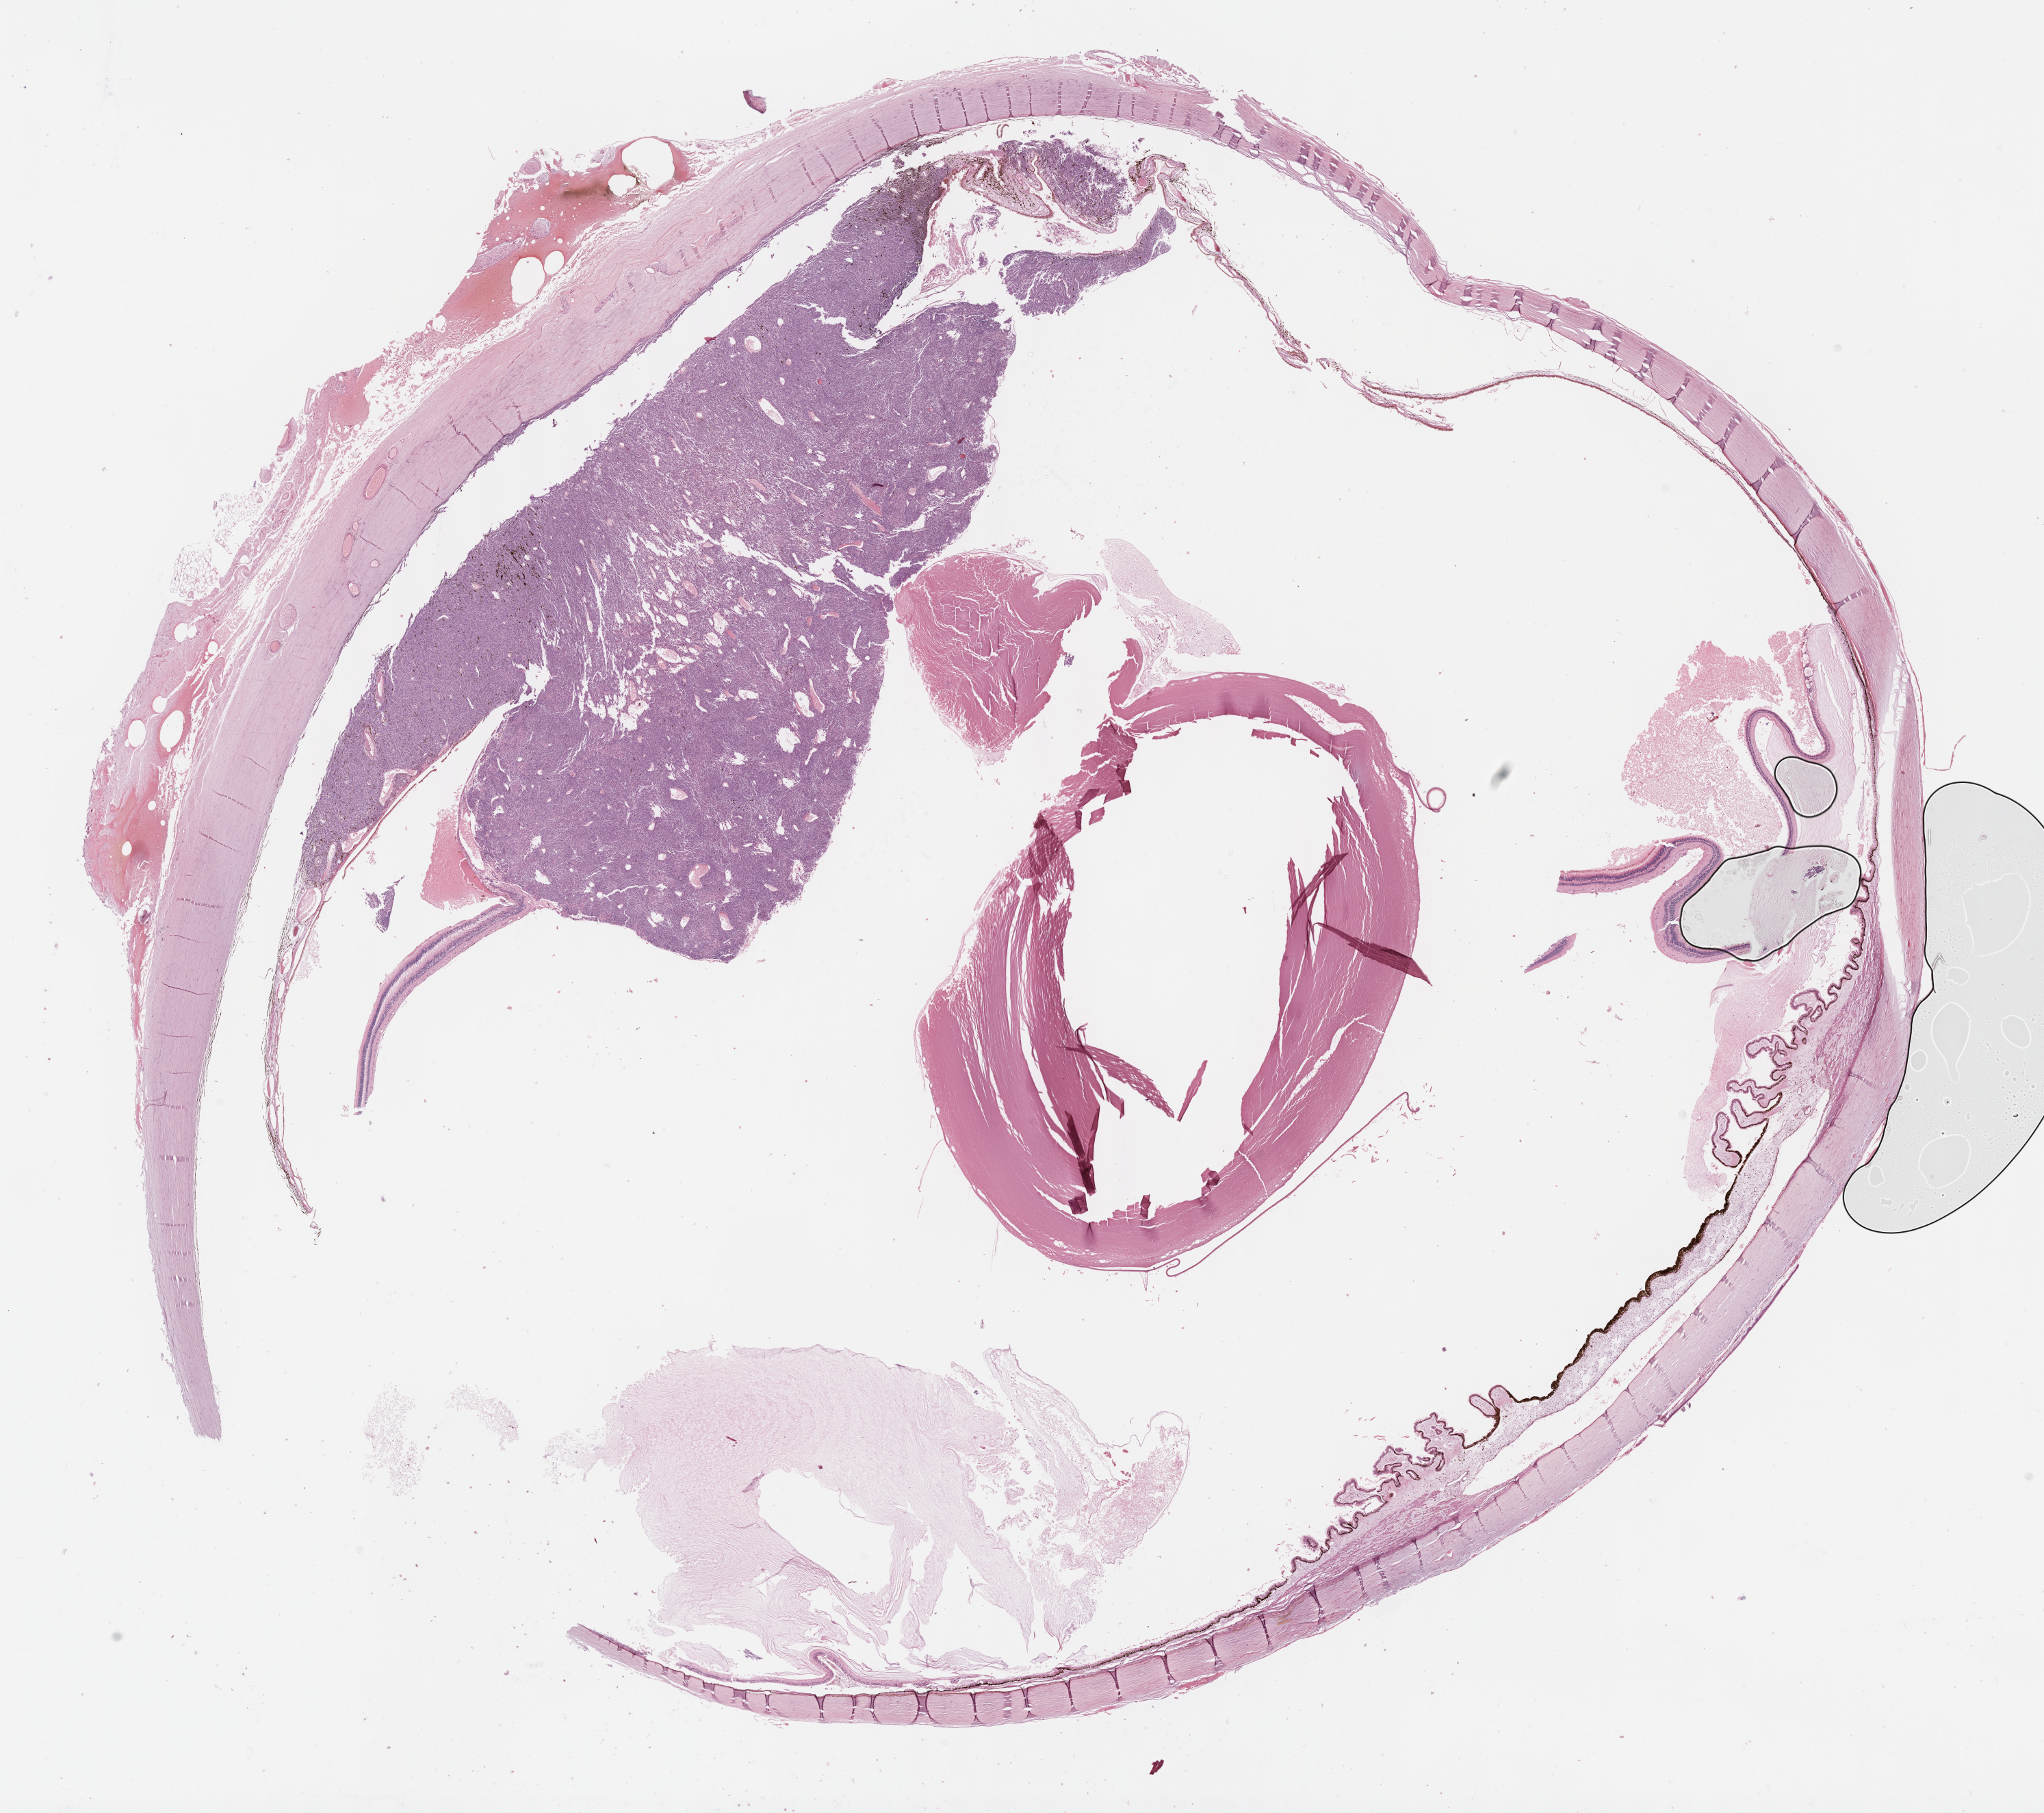
Whole-slide histology image, H&E — a low-resolution overview of the entire scanned area, about 24.2 x 21.4 mm (acquisition: 40x scan). Formalin-fixed paraffin-embedded (FFPE) diagnostic section. Primary tumour sample from the uvea. Patient: female, age at initial diagnosis 78 years.
Histologic diagnosis: Mixed epithelioid and spindle cell melanoma (choroid).